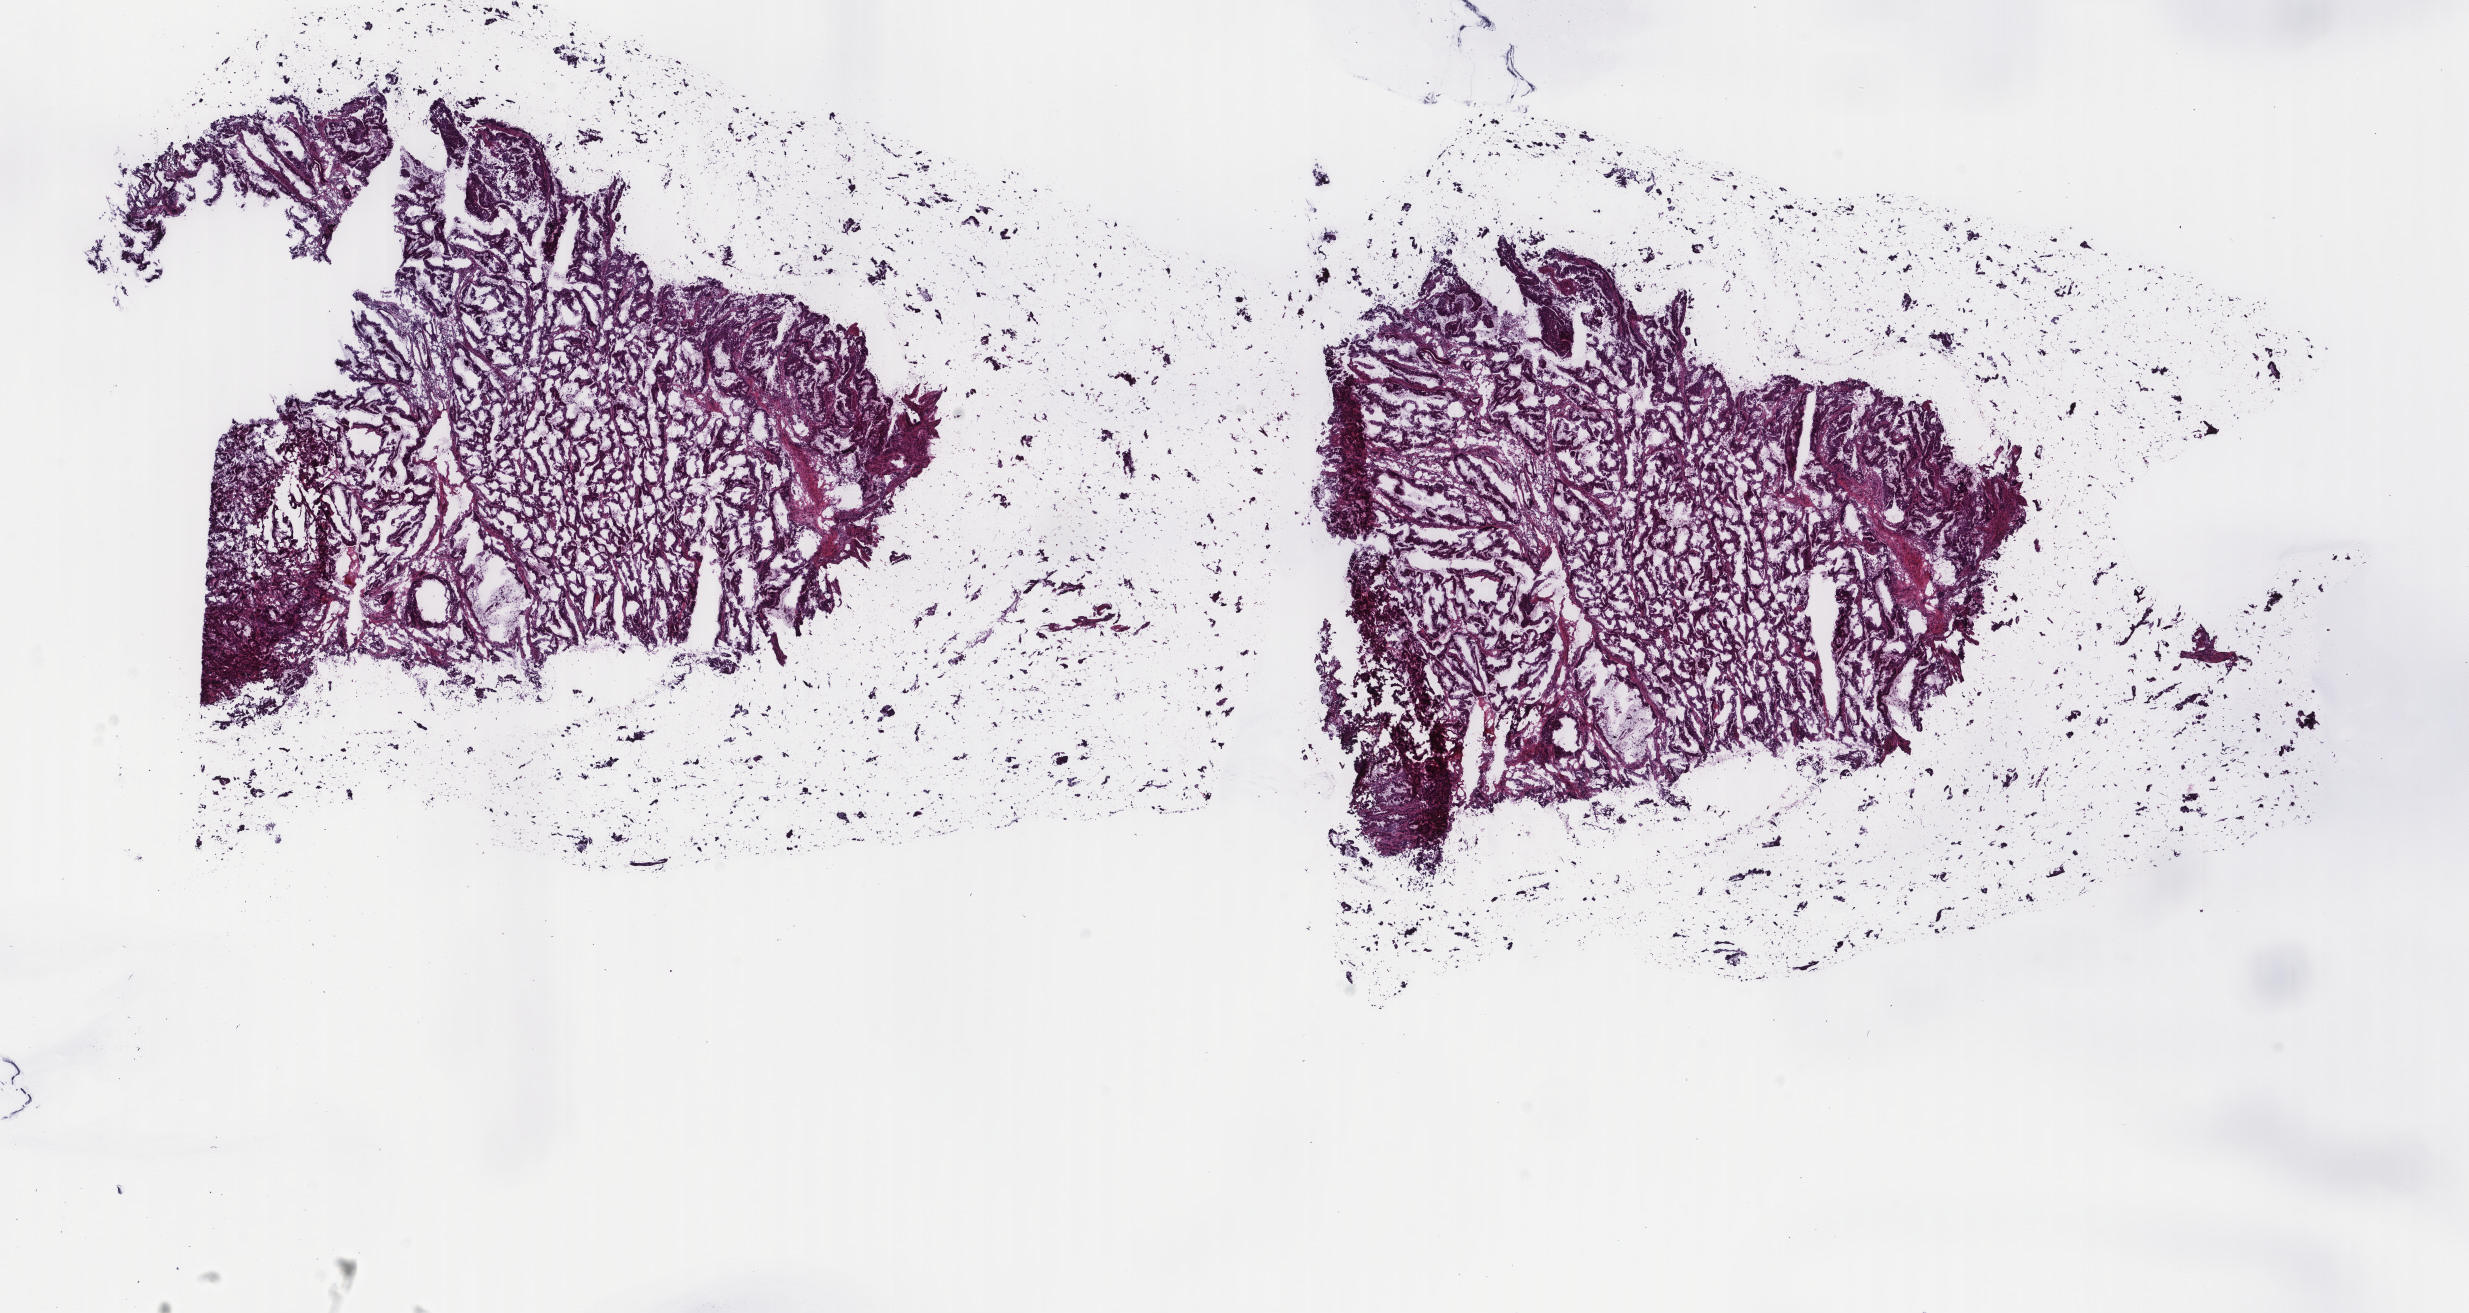
Digitized H&E-stained tissue section (whole slide), shown as a low-resolution overview of the whole scanned area (about 19.6 x 10.4 mm, from a 40x scan); frozen section from the top of the tissue portion; primary tumour sample from the colon. Male patient; age at initial diagnosis 80 years. Composition of this section per pathologist review: tumour cells 100%, tumour nuclei 70%, normal cells 0%, stromal cells 0%, necrosis 0%. Inflammatory infiltration, as recorded: lymphocyte infiltration 0%, monocyte infiltration 0%, neutrophil infiltration 0%.
Lymph nodes positive (case pathology): 0 of 15 examined. AJCC pathologic stage: IIA. TNM: T3 N0 M0. Pathologic diagnosis: Adenocarcinoma, NOS (cecum).